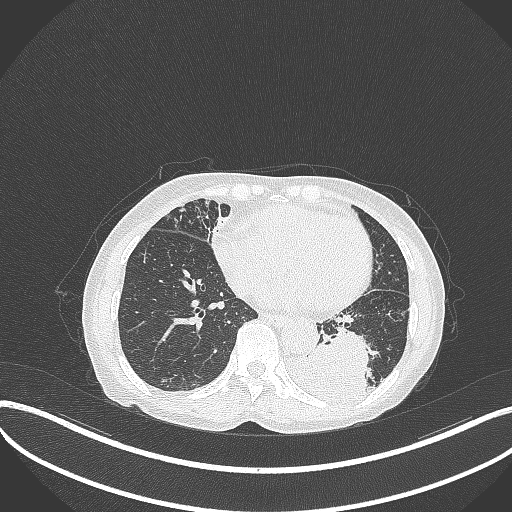
Chest CT, one axial slice. Position 104 of 370 along the scan axis. Reconstruction kernel B70f. Lung window (W 1500 / L -600 HU). 1 mm slice thickness. 512 × 512 image matrix, field of view 400 × 400 mm. Female patient, age 78 years. From the clinical record (not read from this slice): clinical TNM (as recorded): T3 N0 M1.
Structures marked on this image (rectangle marked by the reading radiologist):
- lung tumour (recorded histology: squamous cell carcinoma): bounding box [x1, y1, x2, y2] px = [282, 332, 376, 410]